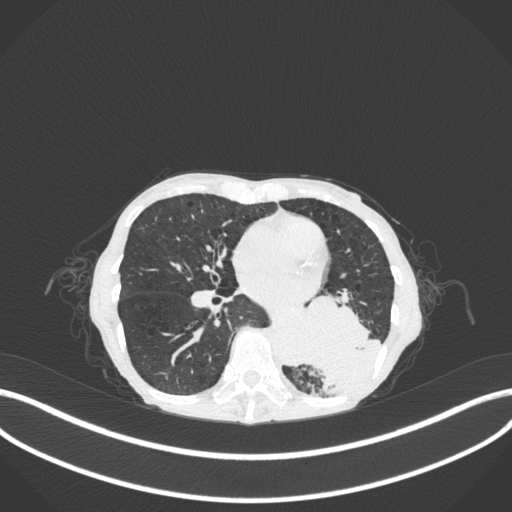
Chest CT, one axial slice; slice 122 of 347 in the series (ordered by position); reconstruction kernel B31f; 120 kVp; lung window (W 1500 / L -600 HU); 1 mm slice thickness; 512 × 512 image matrix. Female patient, age 70 years. Case-level facts recorded for this patient, not image findings: clinical TNM (as recorded): T3 N0 M0.
Outlined on this slice (bounding box drawn by a radiologist):
- lung tumour (recorded histology: small cell carcinoma): box from (x=291, y=286) to (x=387, y=399) px